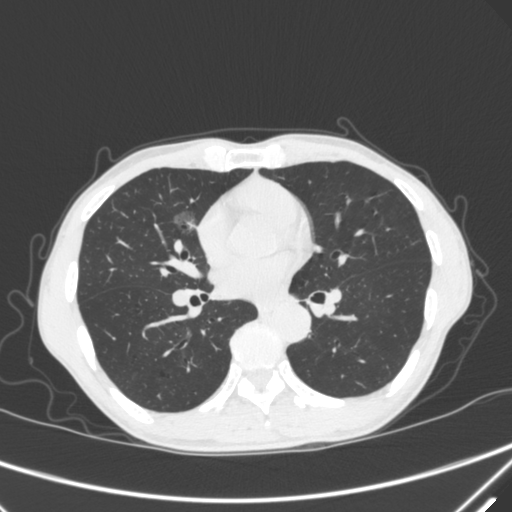
Chest CT, one axial slice. Slice 166 of 340 in the series (ordered by position). 120 kVp. Lung window (W 1500 / L -600 HU). 512 × 512 image matrix, field of view 350 × 350 mm. Male patient, age 67 years. Case-level facts recorded for this patient, not image findings: clinical TNM (as recorded): T1c N0 M0; histopathological grade: G1-2.
Structures marked on this image (bounding box drawn by a radiologist):
- lung tumour (recorded histology: adenocarcinoma): bounding box [x1, y1, x2, y2] px = [164, 202, 202, 248]